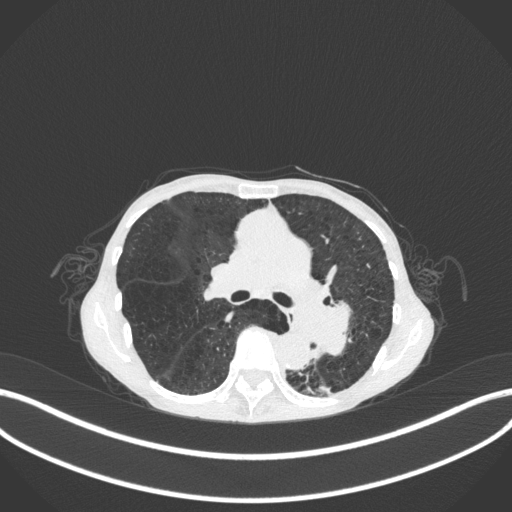
Chest CT, one axial slice. Slice 167 of 347 in the series (ordered by position). Reconstruction kernel B31f. Lung window (W 1500 / L -600 HU). 512 × 512 image matrix, field of view 400 × 400 mm. Female patient, age 70 years. Case-level facts recorded for this patient, not image findings: clinical TNM (as recorded): T3 N0 M0.
Annotated regions visible in this slice (bounding box drawn by a radiologist):
- lung tumour (recorded histology: small cell carcinoma): bounding box <308,284,368,364> (left, top, right, bottom; pixels)